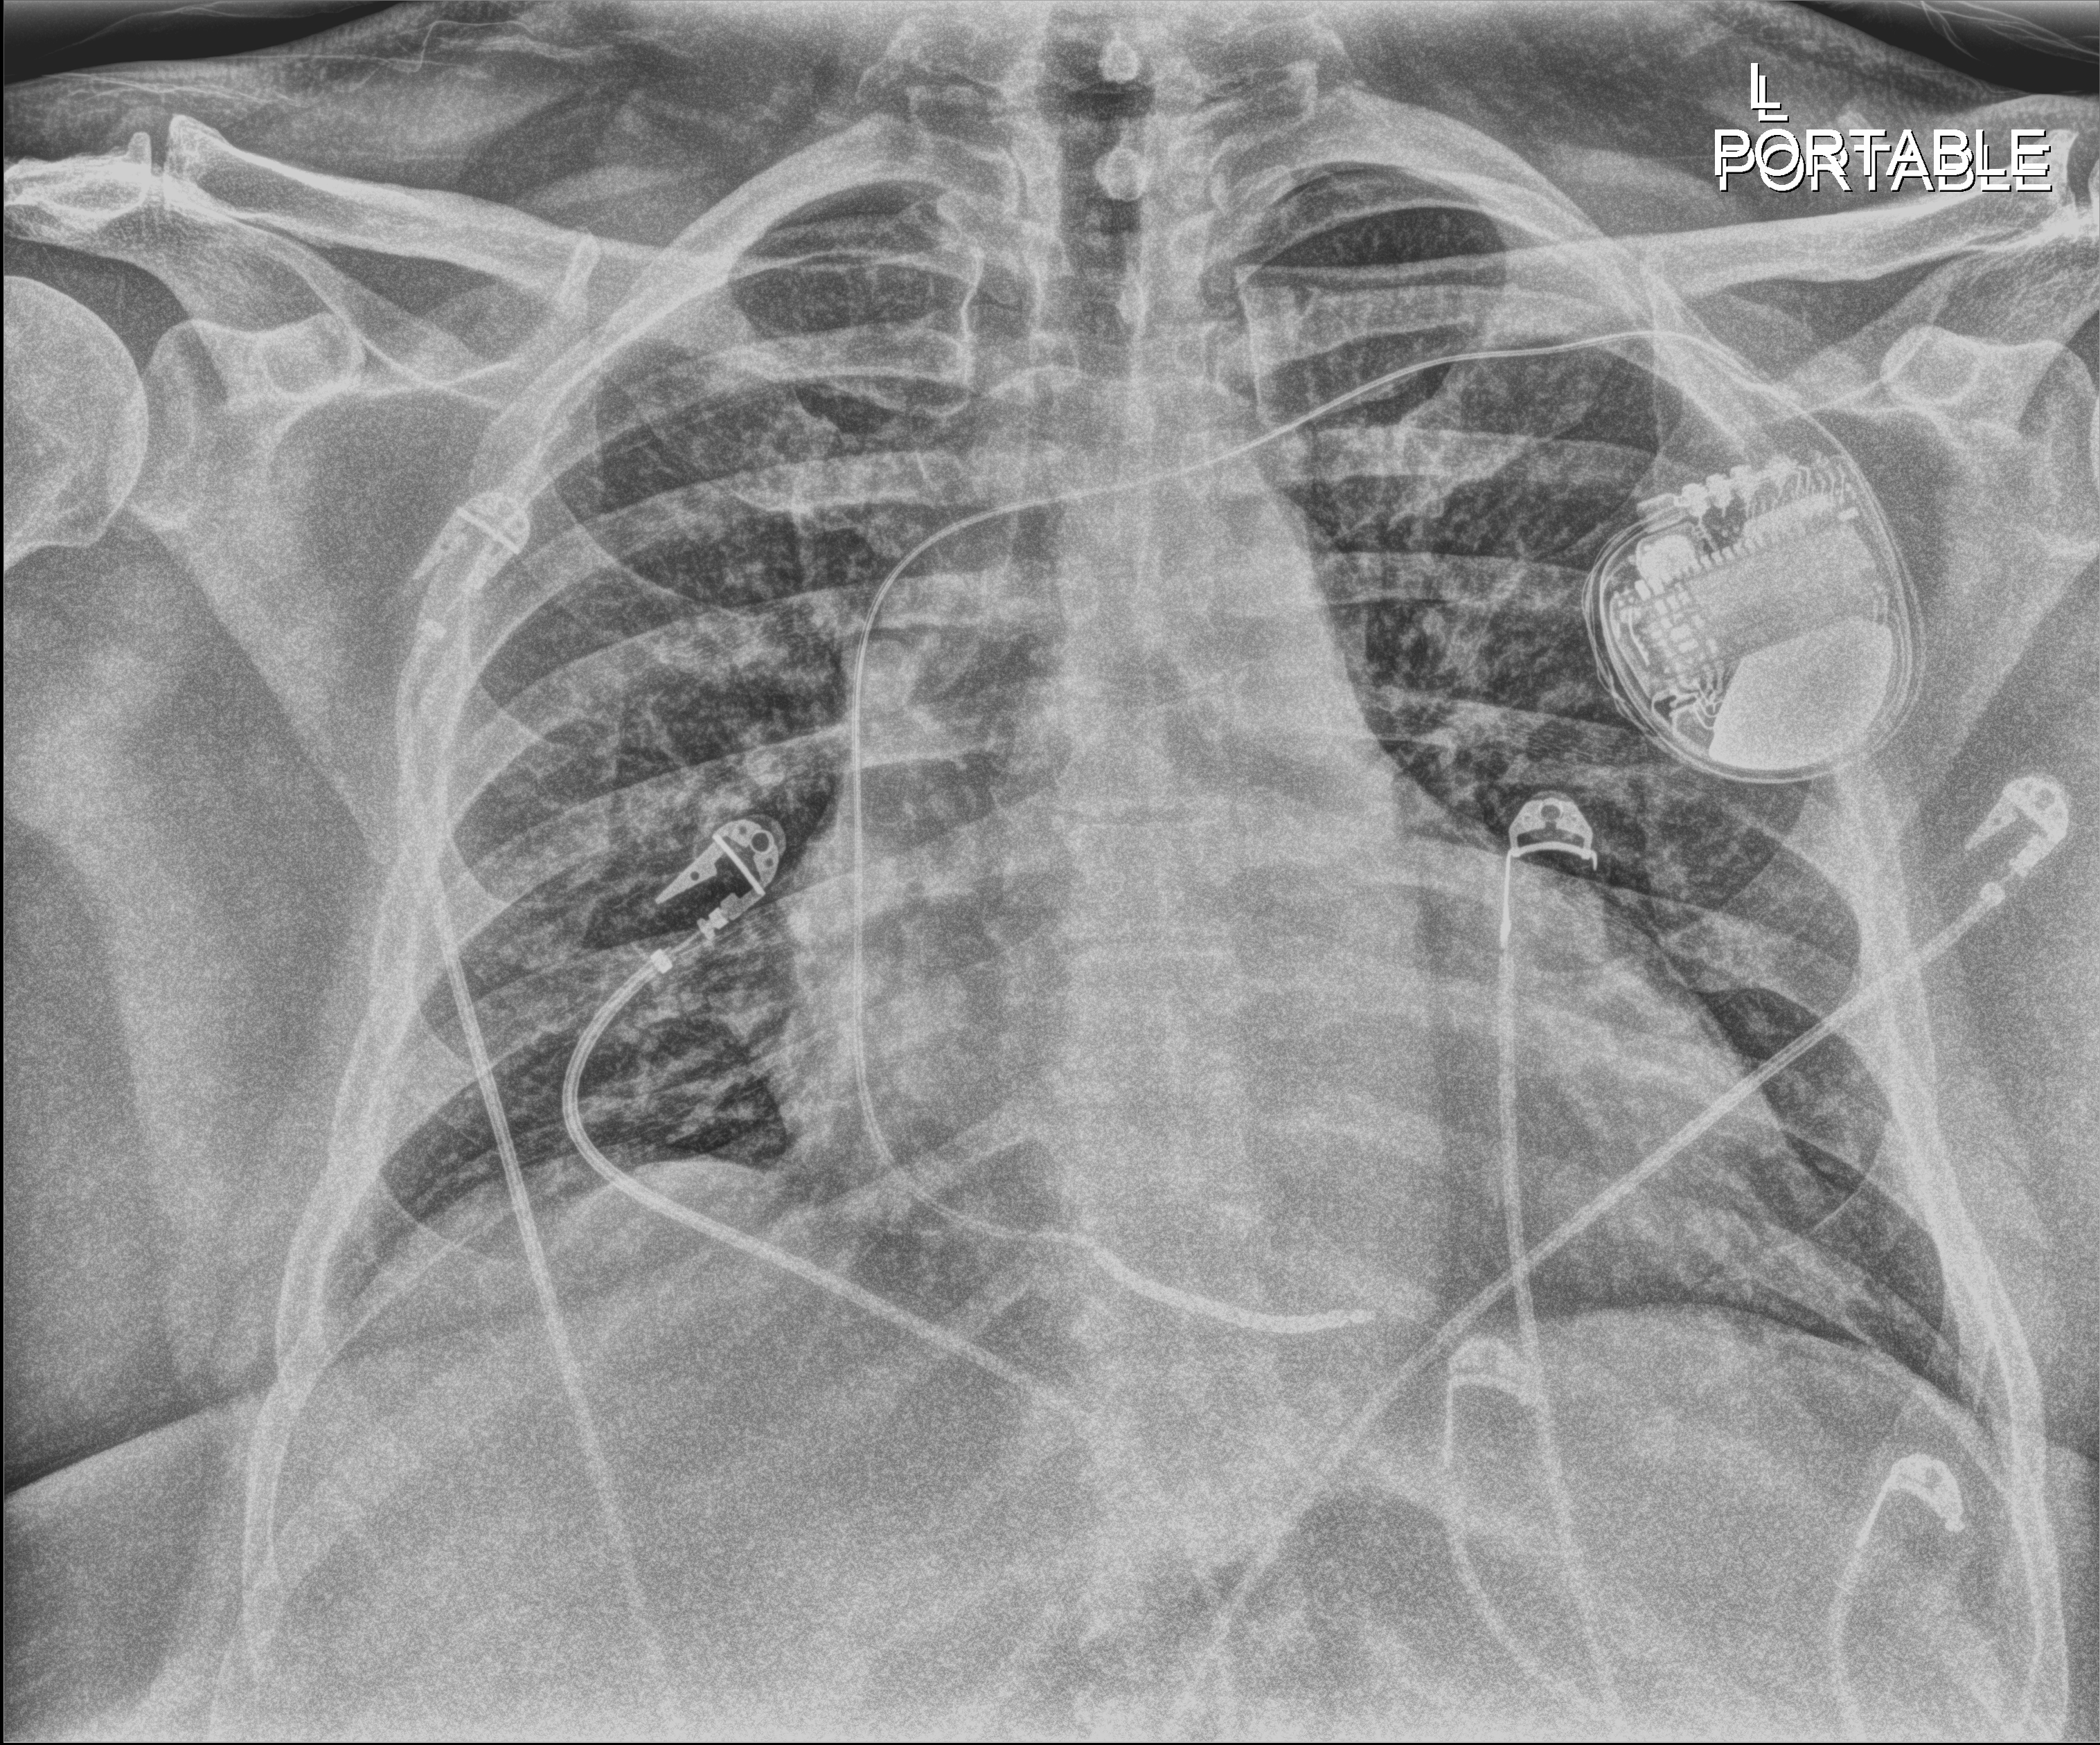
Chest radiograph (digital radiography). Patient hospitalised with COVID-19; male, aged 18–59 years.
Admission-level facts for this patient (not findings on this image; timing relative to this image not recorded):
- smoking status (admission record): never
- admitted to intensive care during this hospital stay: yes
- mechanically ventilated during this hospital stay: no